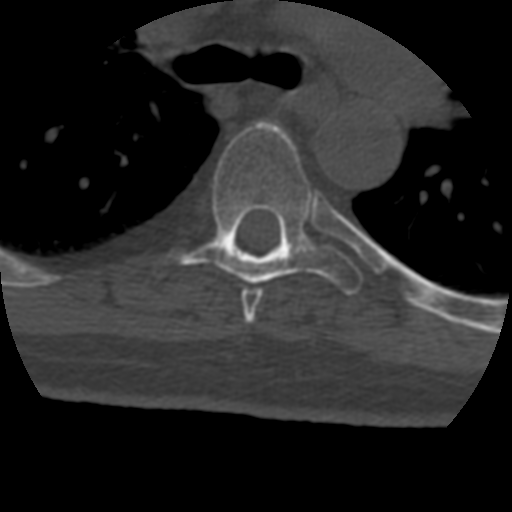
CT including the spine, one axial slice. Slice 303 of 399 in the series (ordered by position). 120 kVp. Bone window (W 1800 / L 400 HU). 1.25 mm slice thickness. 512 × 512 image matrix, field of view 160 × 160 mm. Patient age 69 years. Case-level facts recorded for this patient, not image findings: primary cancer: prostate.
Annotated regions visible in this slice (semi-automatic segmentation, software-assisted and operator-edited):
- T5 vertebra: bounding box <241,289,263,324> (left, top, right, bottom; pixels)
- T6 vertebra: <155,122,364,293>